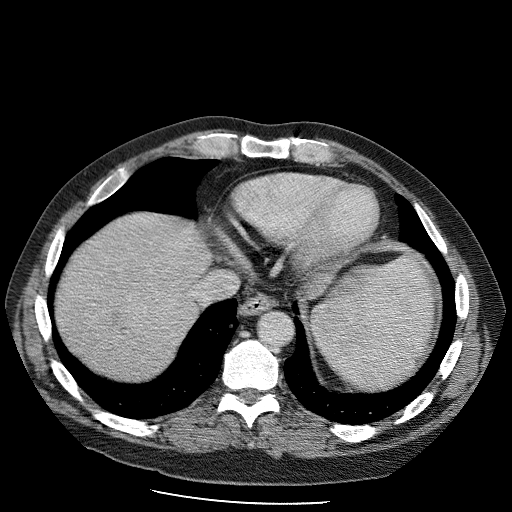
Contrast-enhanced abdominal CT (liver protocol), one axial slice; position 90 of 98 along the scan axis; reconstruction kernel STANDARD; soft-tissue window (W 400 / L 40 HU); 2.5 mm slice thickness; 512 × 512 image matrix, field of view 400 × 400 mm. Case-level facts recorded for this patient, not image findings: diagnosis: hepatocellular carcinoma (patient treated with transarterial chemoembolisation; whether this scan precedes or follows treatment is not stated here); TNM stage (as recorded): Stage-II; Child-Pugh class: B; tumour differentiation: moderately differentiated; tumour nodularity: uninodular.
Outlined on this slice (semi-automatically segmented with operator editing):
- liver parenchyma outside the tumour (the mass and vessels are separate outlines, so this box may not span the whole liver): bounding box [x1, y1, x2, y2] px = [58, 212, 210, 374]
- mass: [105, 299, 135, 341]